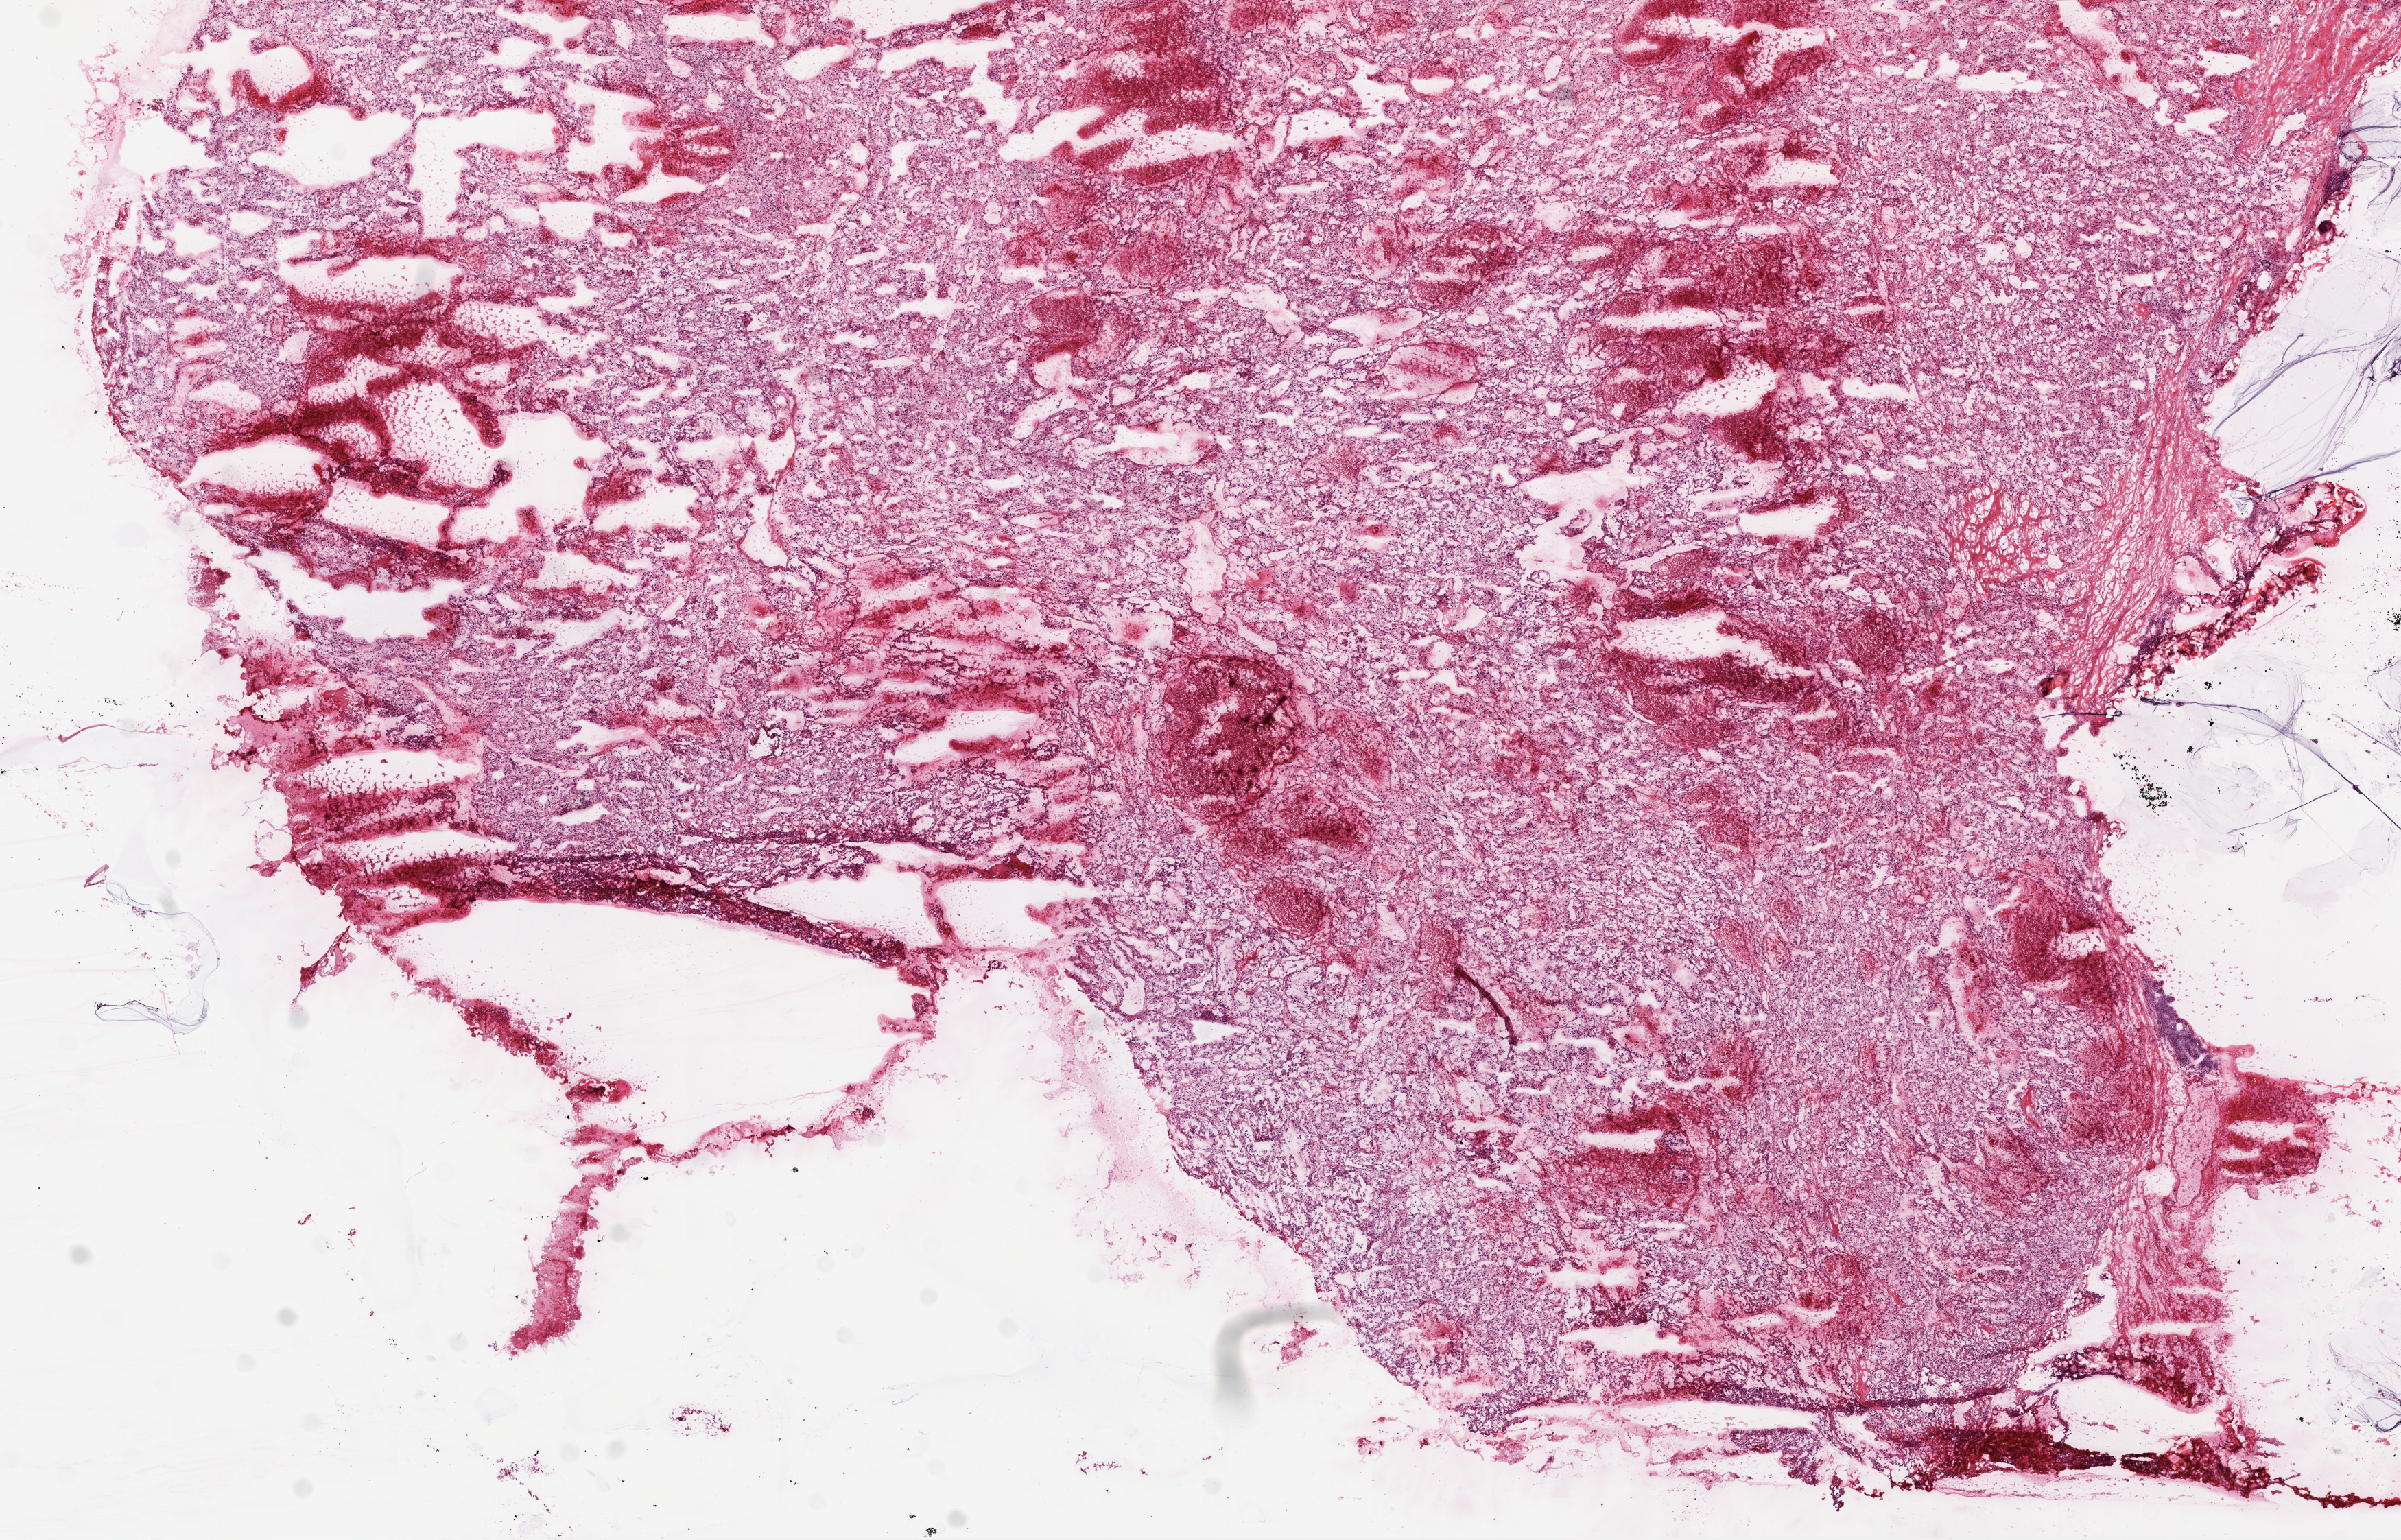
Whole-slide histology image, H&E — a low-resolution overview of the entire scanned area, about 14.0 x 9.0 mm (acquisition: 20x scan). Frozen section. Kidney, primary tumour sample. Female patient; age at initial diagnosis 75 years. Histologic grade: G3 (poorly differentiated). Pathologist review of this section (percent, as recorded): tumour cells 75%, tumour nuclei 85%, normal cells 0%, stromal cells 5%, necrosis 20%.
TNM: T3a N0 M0. AJCC pathologic stage: III (7th edition). Histologic diagnosis: Clear cell adenocarcinoma, NOS.